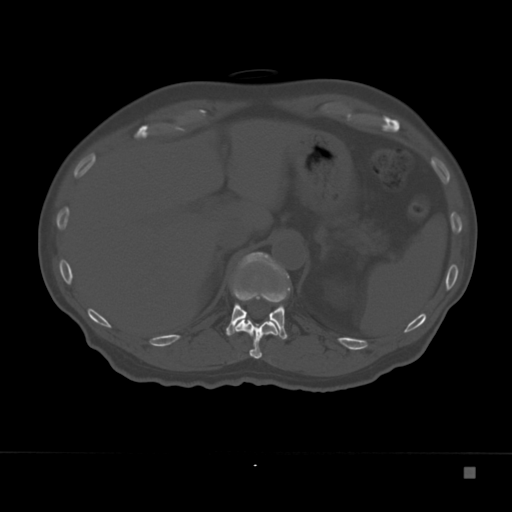
CT including the spine, one axial slice; slice 142 of 332 in the series (ordered by position); reconstruction kernel Br40s; 120 kVp; bone window (W 1800 / L 400 HU); 1.5 mm slice thickness; 512 × 512 image matrix. Male patient, age 72 years. From the clinical record (not read from this slice): primary cancer: skeletal.
Outlined on this slice (semi-automatic segmentation, software-assisted and operator-edited):
- T11 vertebra: bounding box <234,297,282,359> (left, top, right, bottom; pixels)
- T12 vertebra: <226,252,290,339>